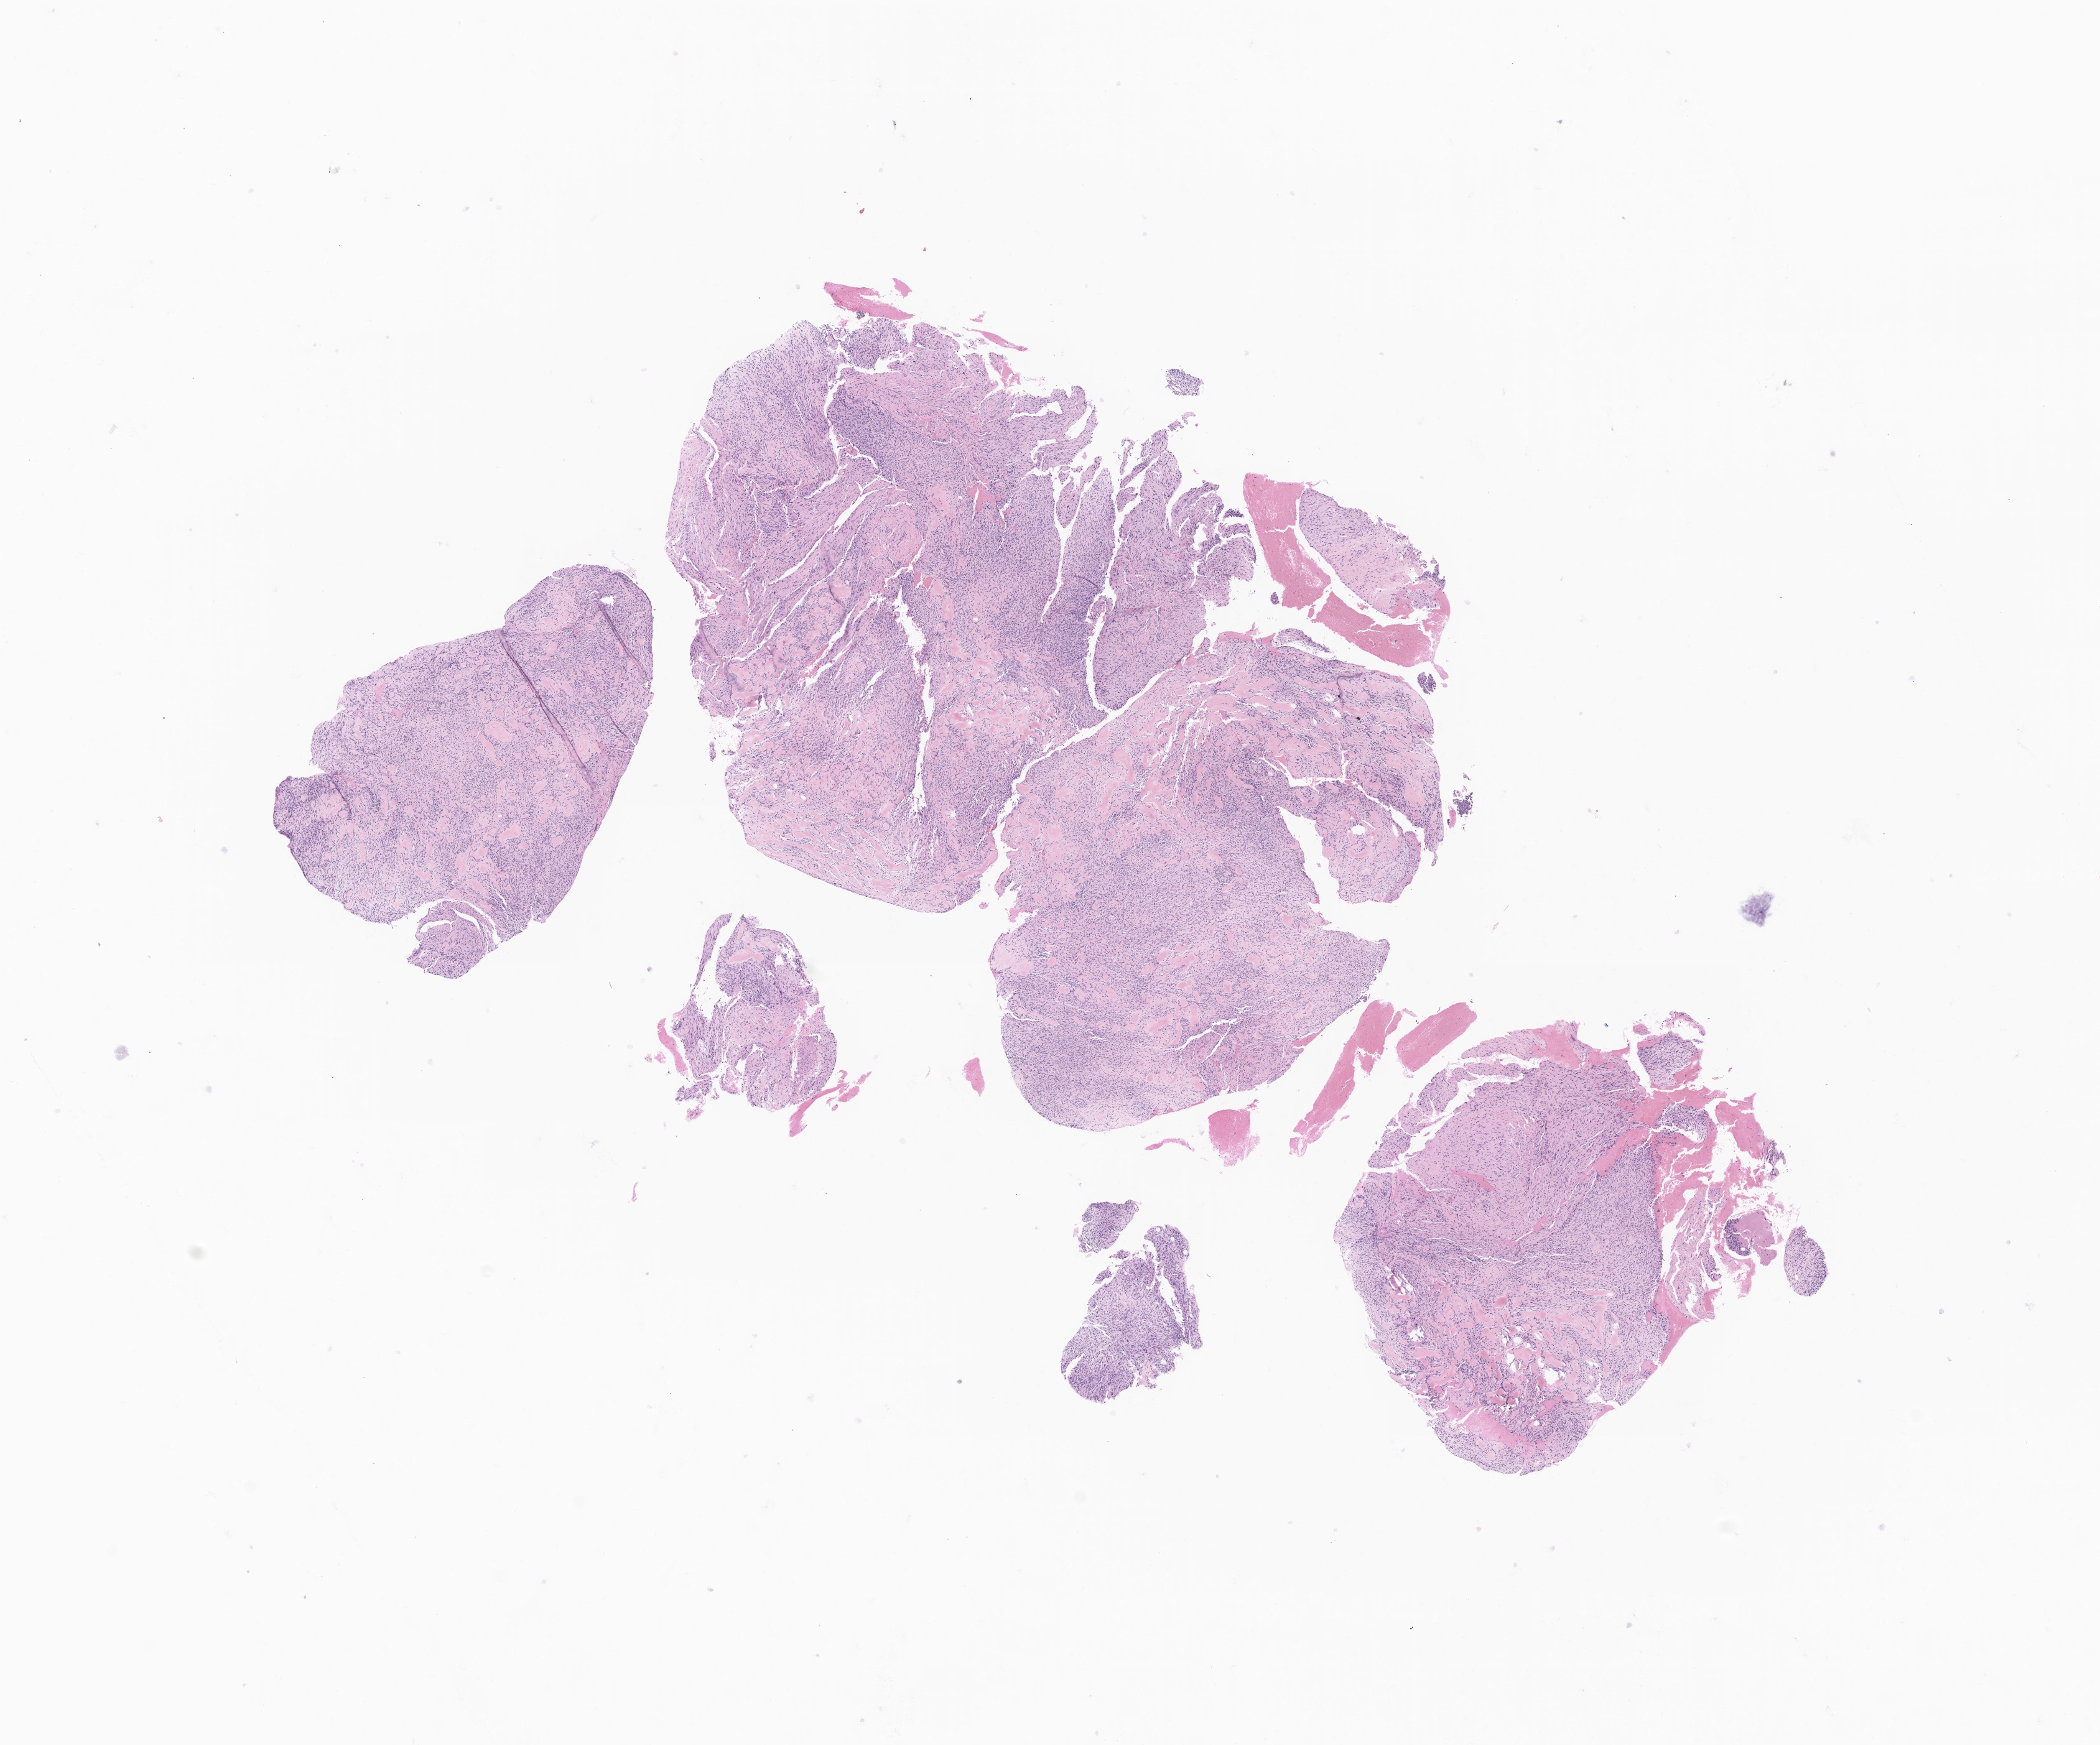
Haematoxylin and eosin whole-slide image of tumor tissue from the lower limb, shown as a low-resolution overview of the whole scanned area (about 14.2 x 11.8 mm), FFPE section. Female patient, age 204 months (17 years).
- diagnosis (ICD-O-3 morphology term): Sarcoma, NOS